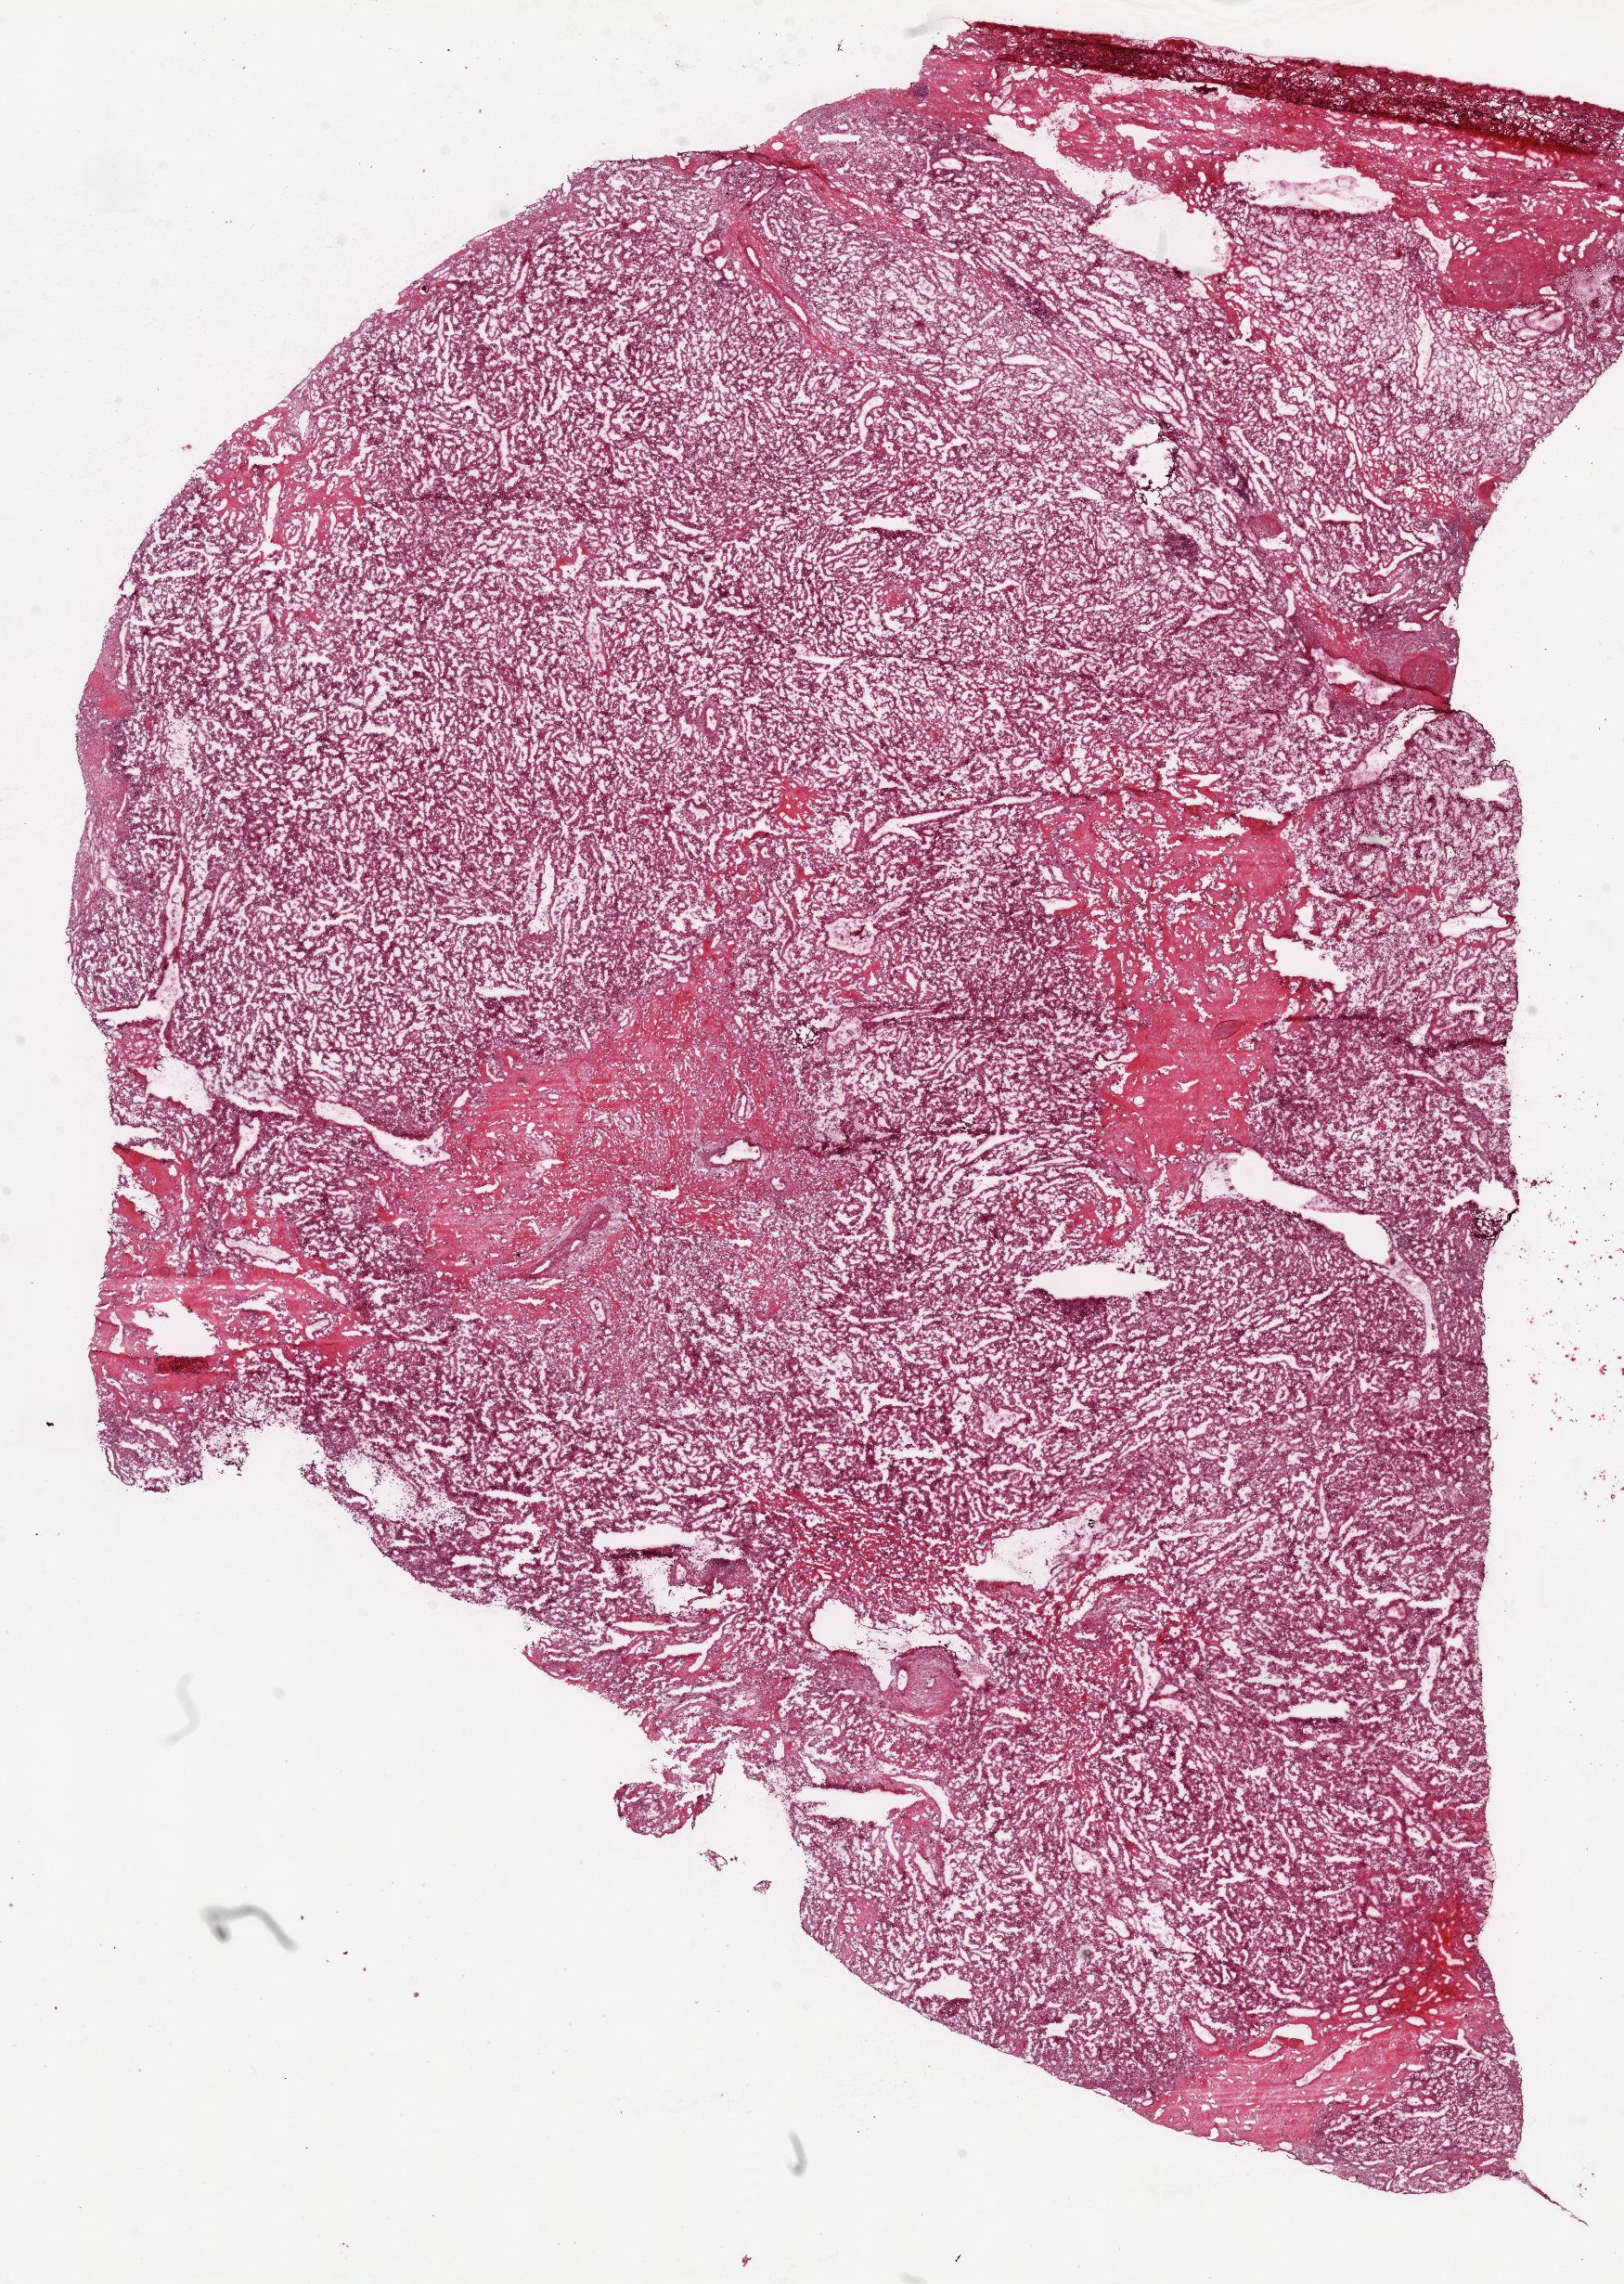
H&E whole-slide image, shown as a low-resolution overview of the whole scanned area (about 14.0 x 19.7 mm). Frozen section. Kidney, primary tumour sample. Male, age 53 years at initial diagnosis. Histologic grade: G2 (moderately differentiated). Pathologist review of this section (percent, as recorded): tumour cells 85%, tumour nuclei 85%, normal cells 5%, stromal cells 10%, necrosis 0%.
Histologic diagnosis: Clear cell adenocarcinoma, NOS. AJCC pathologic stage: I. Laterality: left.